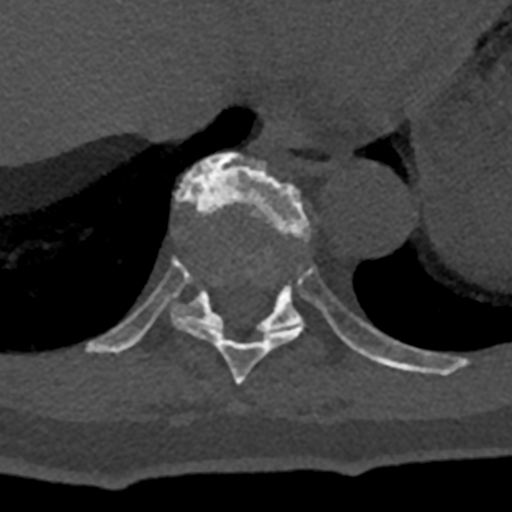
CT including the spine, one axial slice; position 631 of 797 along the scan axis; reconstruction kernel Br40s/3; bone window (W 1800 / L 400 HU); 0.5 mm slice thickness; 512 × 512 image matrix, field of view 160 × 160 mm. Patient: male, 74 years. From the clinical record (not read from this slice): primary cancer: renal.
Outlined on this slice (semi-automatically segmented with operator editing):
- T10 vertebra: bounding box [x1, y1, x2, y2] px = [85, 152, 432, 374]
- T9 vertebra: [173, 256, 303, 385]